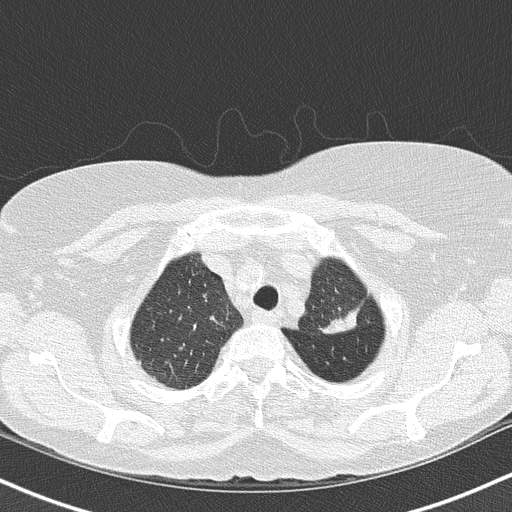
Axial slice from a low-dose chest CT screening exam. Third screening round (two years after baseline). Lung window (W 1500 / L -600 HU). 2 mm slice thickness. Slice 128 of 147 in the series. Female, age 68 years at enrolment. Former smoker at enrolment.
Expert-annotated lung lesion, bounding box (x1, y1, x2, y2) in pixels: (286, 241, 378, 347). Reader record for this screening exam (exam-level; its link to the box is not recorded): non-calcified nodule or mass ≥4 mm, left upper lobe, 5 × 5 mm, poorly defined margins, mixed attenuation, pre-existing on the prior screen: yes; interval growth: yes. Later outcome: lung cancer diagnosed 42 days after this screen — adenocarcinoma, NOS, left upper lobe, poorly differentiated (G3), stage IB (AJCC 6th edition), 50 mm at pathology.